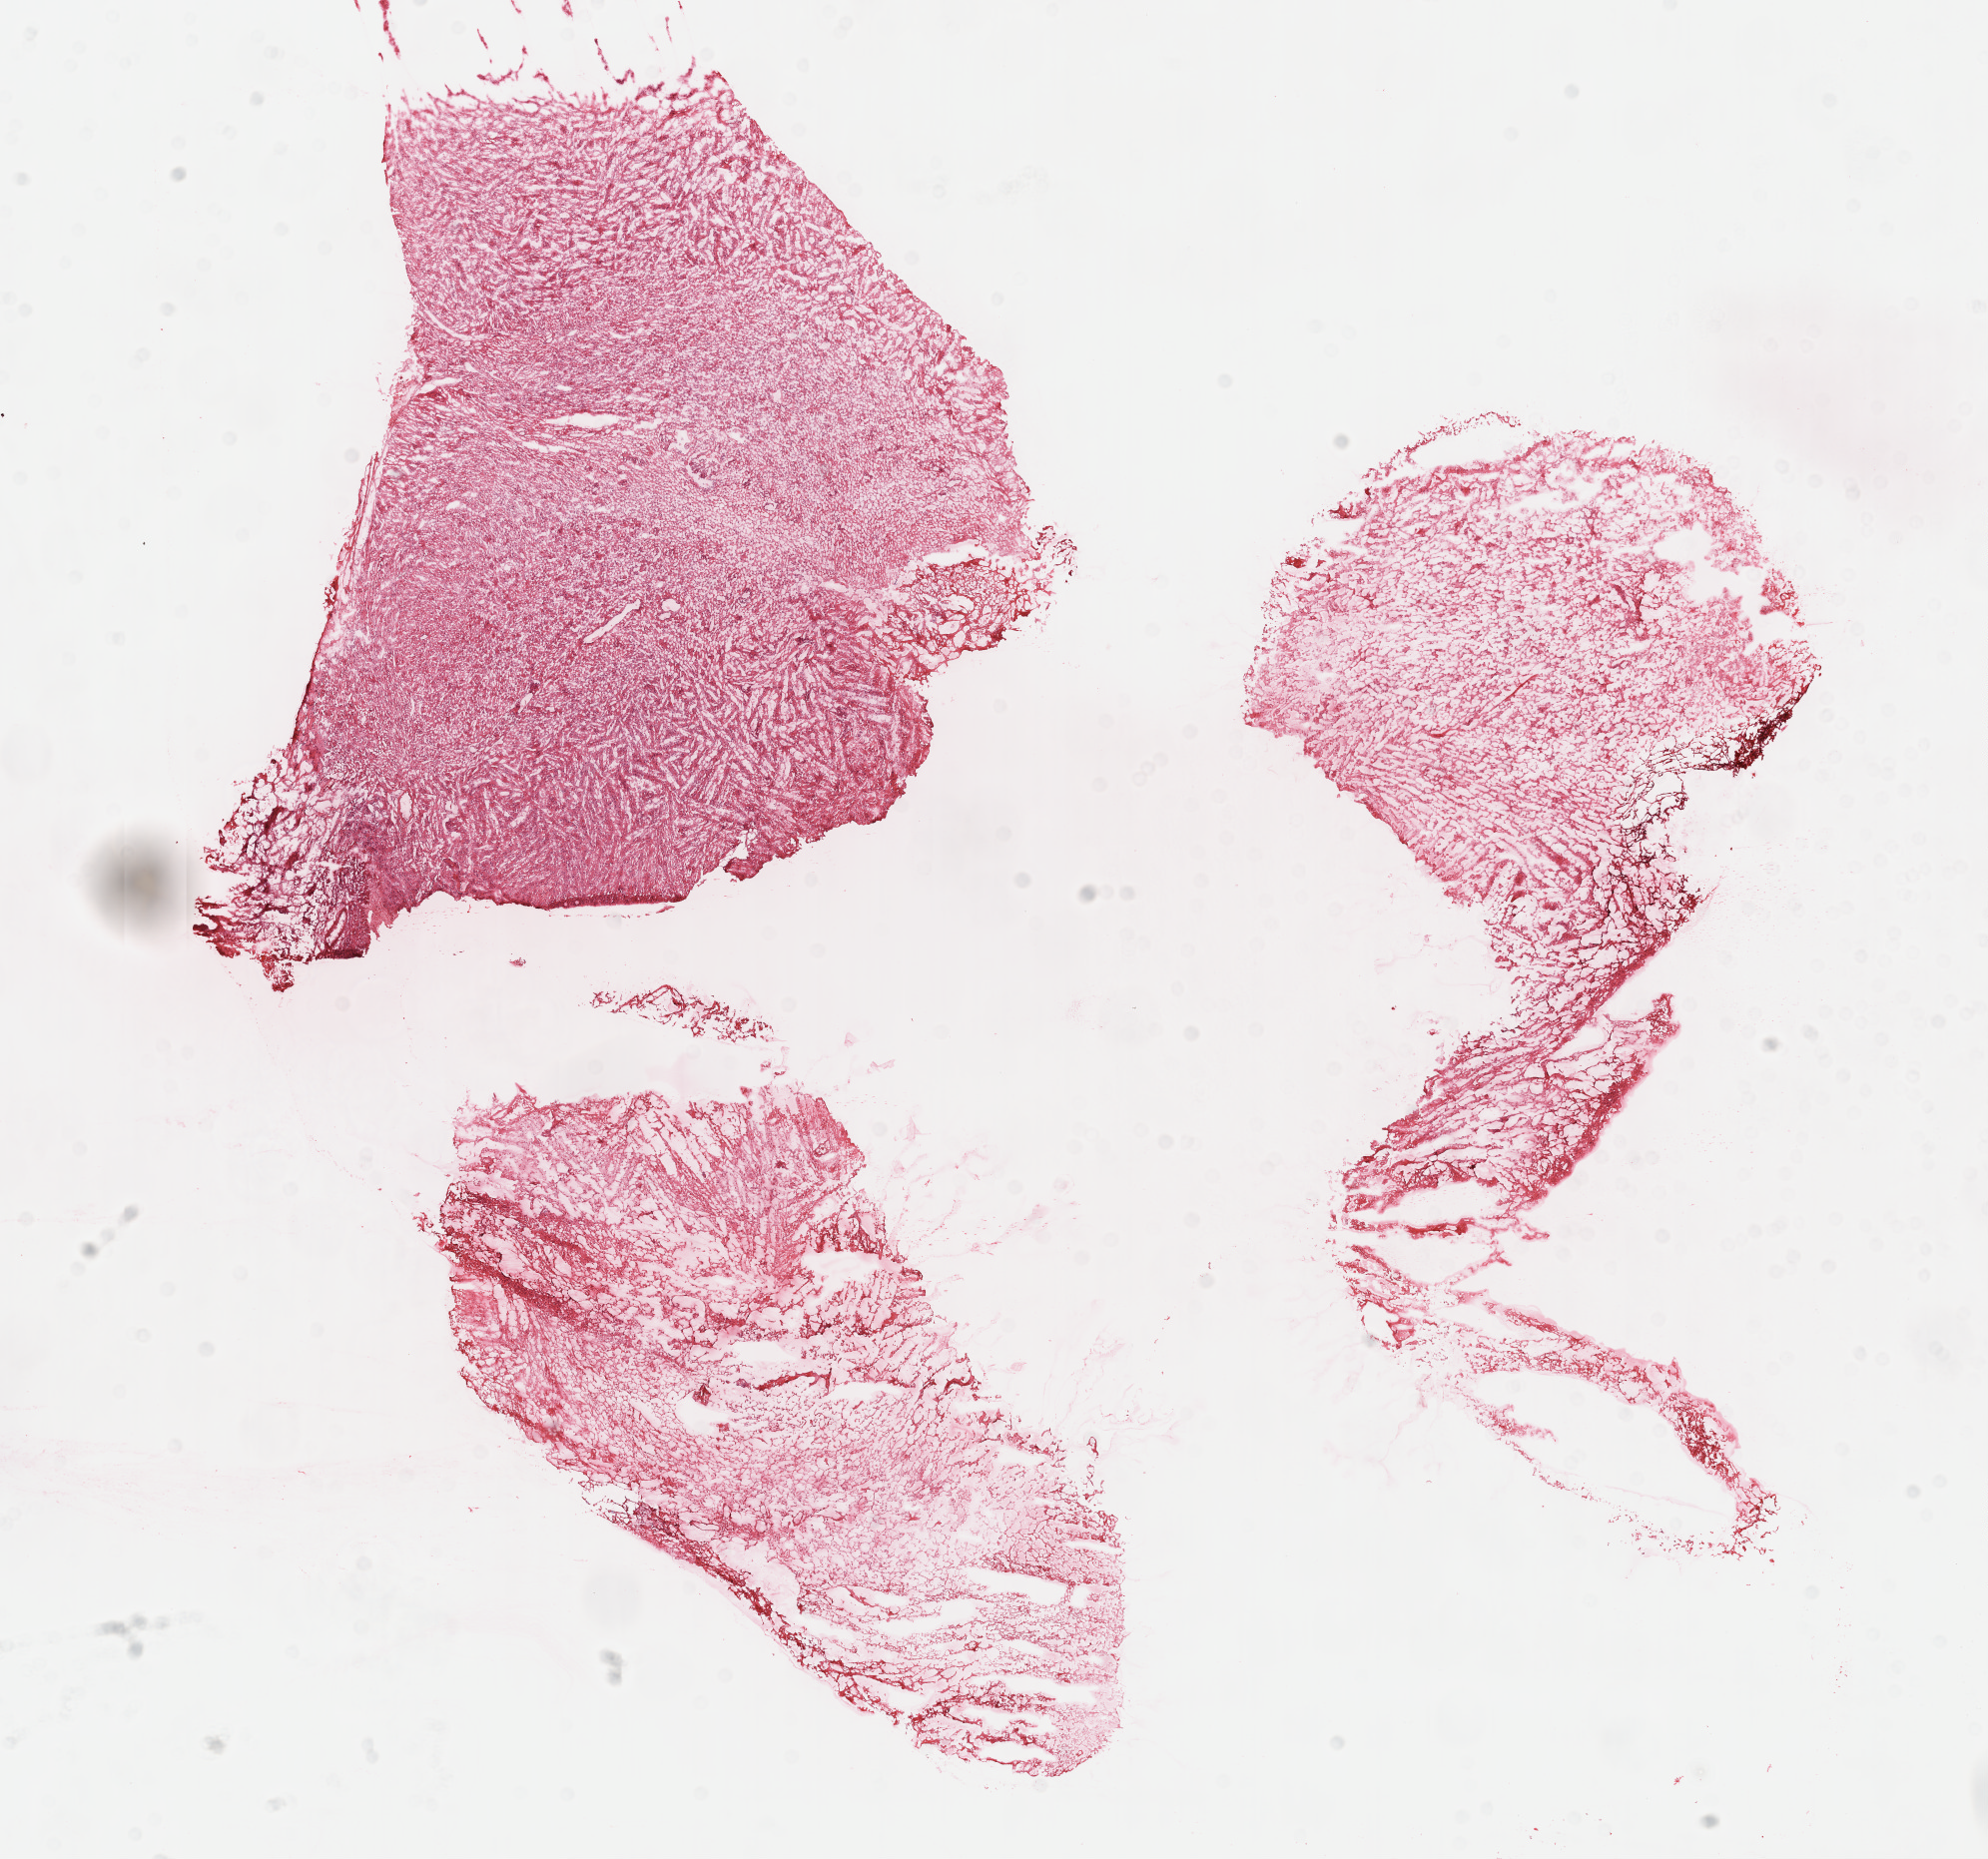
Whole-slide histology image, H&E-stained, low-resolution overview of the scanned area, about 16.1 x 15.1 mm (from a 40x scan). Frozen section from the top of the tissue portion. Sample: primary tumour, brain. Patient: male, age at initial diagnosis 57 years. Pathologist review of this section (percent, as recorded): tumour cells 85%, tumour nuclei 100%, normal cells 0%, stromal cells 0%, necrosis 15%. Infiltration values recorded for this section: lymphocyte infiltration 0%.
• histologic diagnosis: Glioblastoma